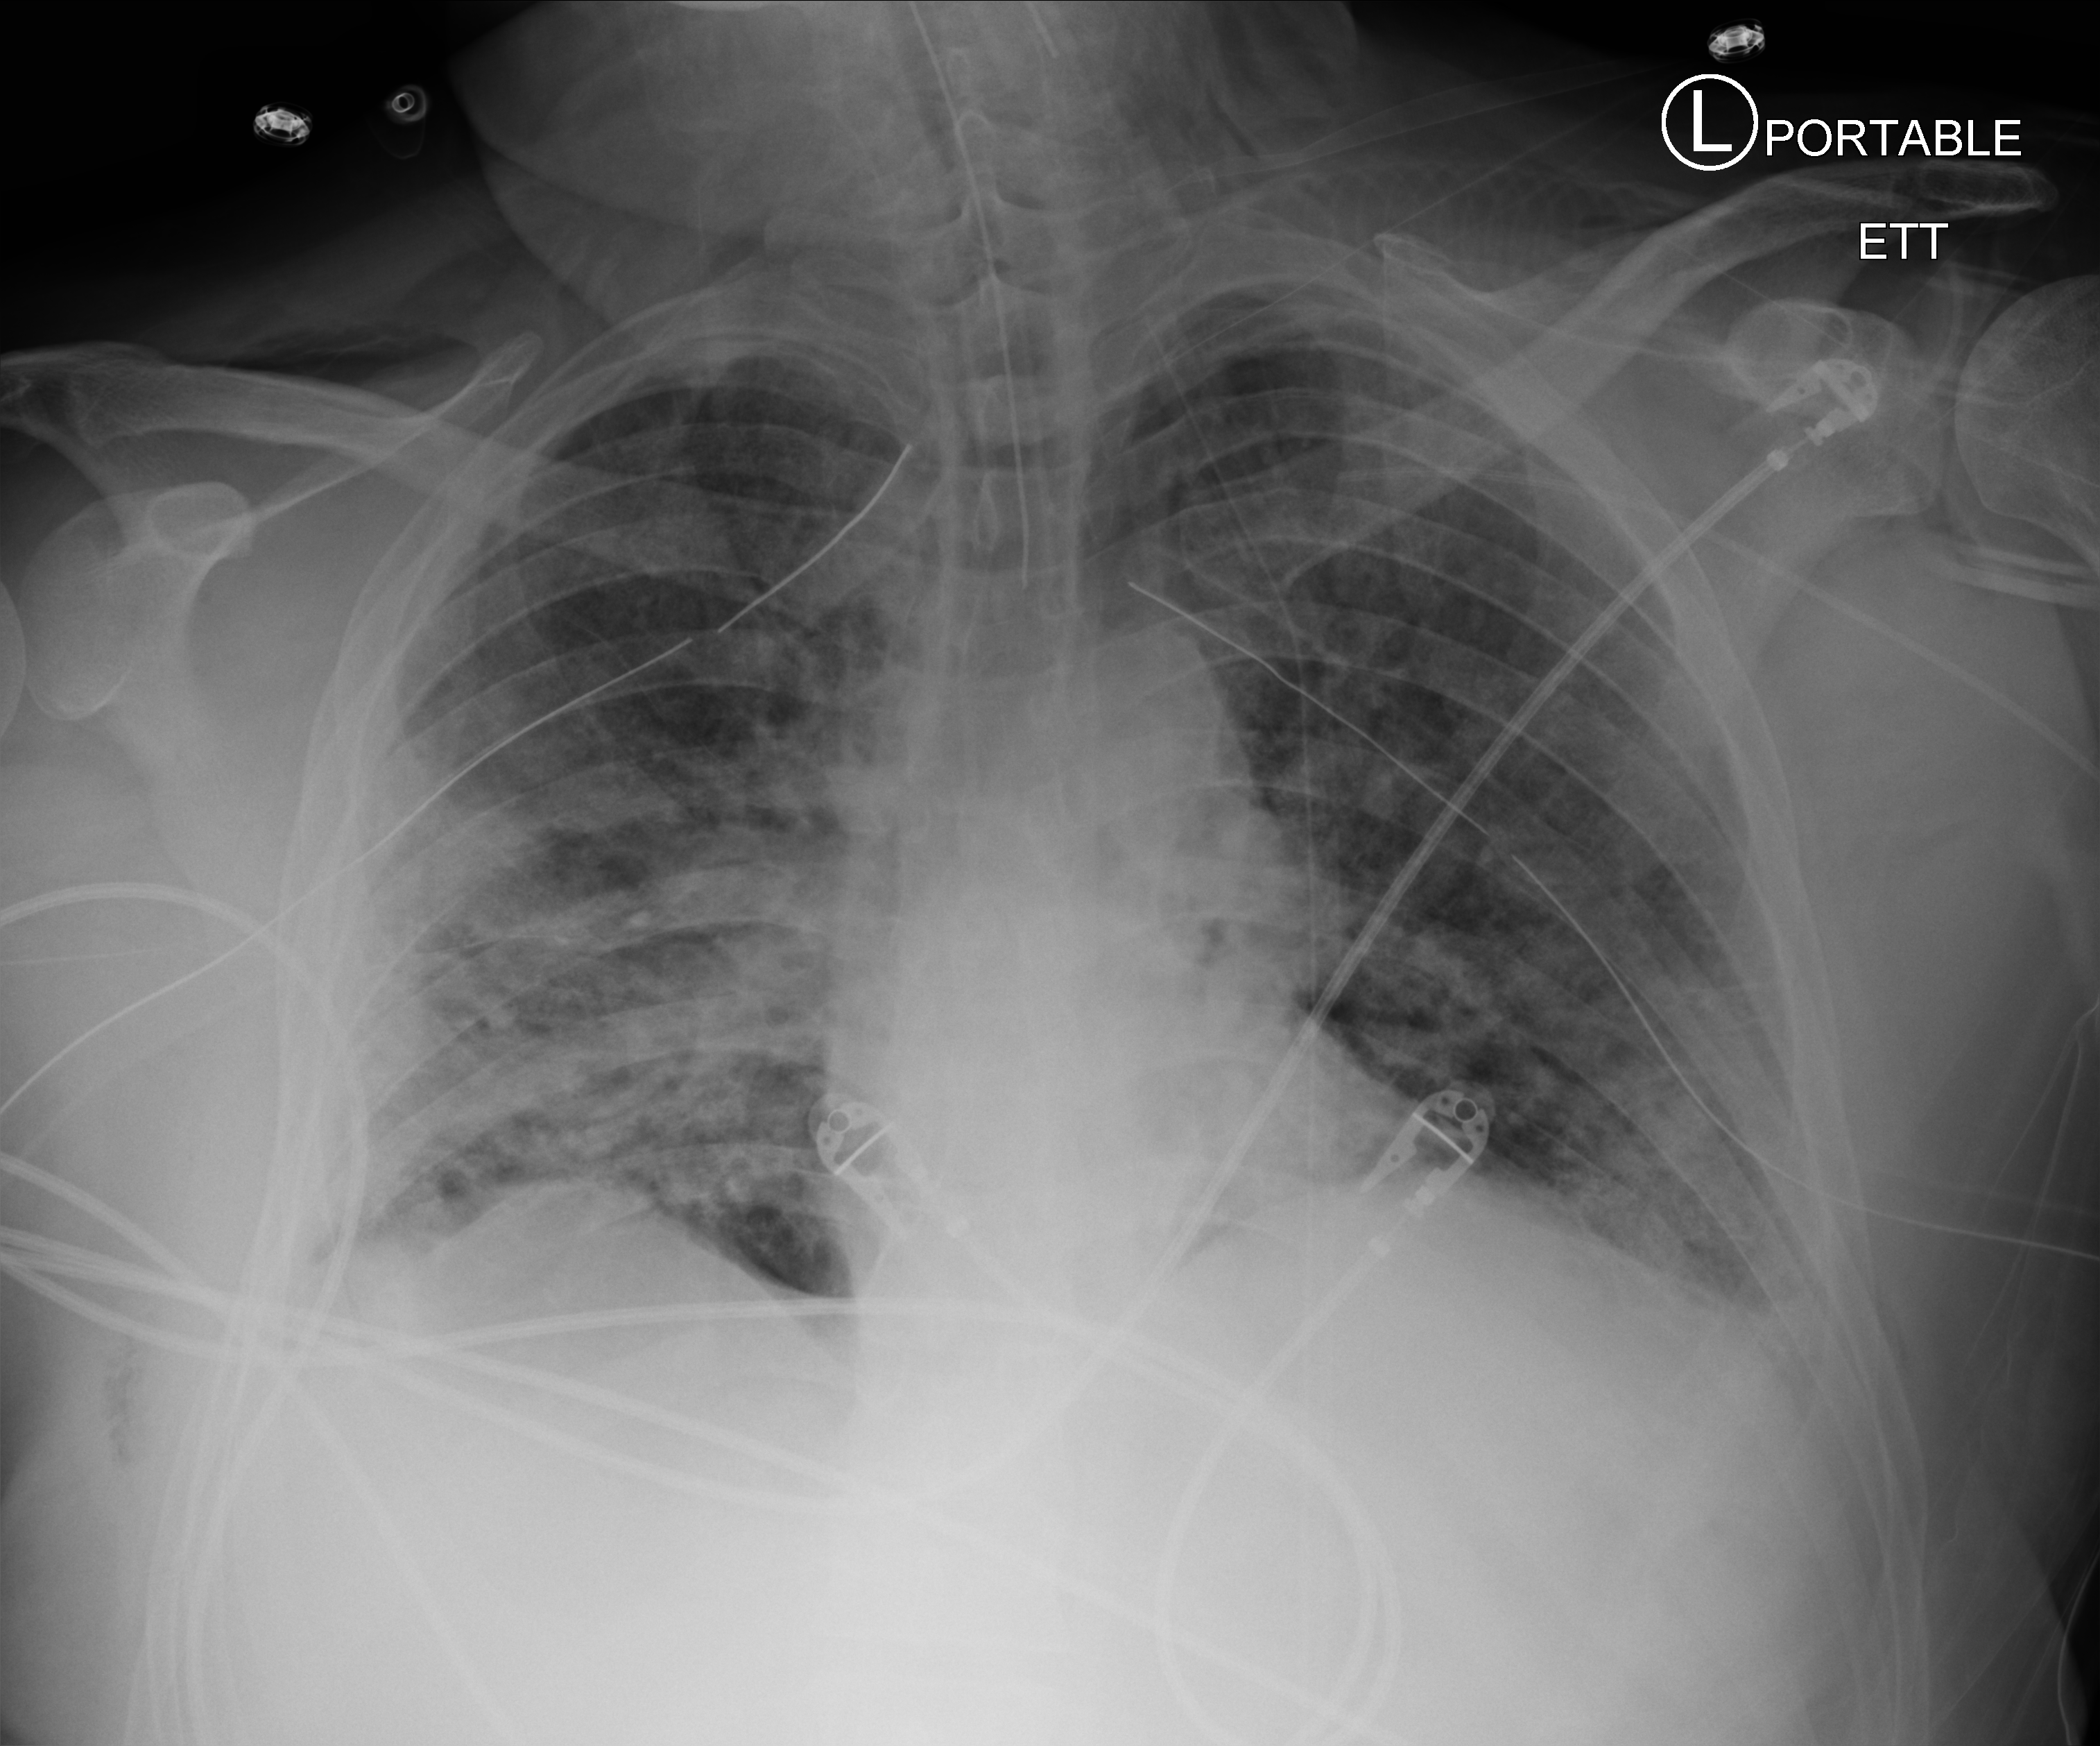
Bedside chest radiograph (computed radiography). Male patient hospitalised with COVID-19, age 18–59 years.
Admission-level facts for this patient (not findings on this image; timing relative to this image not recorded): length of hospital stay: 63 days.